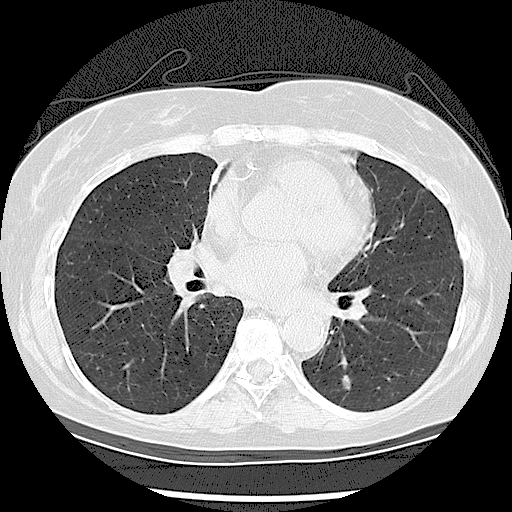
Axial slice from a low-dose chest CT screening exam; first (baseline) screen; lung window (W 1500 / L -600 HU); 120 kVp. Female participant, aged 61 years at enrolment. Current smoker at enrolment.
Lesion marked by an expert reader, box from (x=321, y=363) to (x=374, y=408) px. The screening reader recorded 2 non-calcified nodules or masses ≥4 mm on this exam; which of them this box marks is not recorded. Official screen result: positive, change unspecified: nodule(s) >= 4 mm or enlarging nodule(s), mass(es), or other non-specific abnormalities suspicious for lung cancer. Lung cancer was diagnosed 570 days after this screen (after the second annual screen): adenocarcinoma, NOS, left lower lobe, moderately differentiated (G2), stage IA (AJCC 6th edition), 18 mm at pathology.